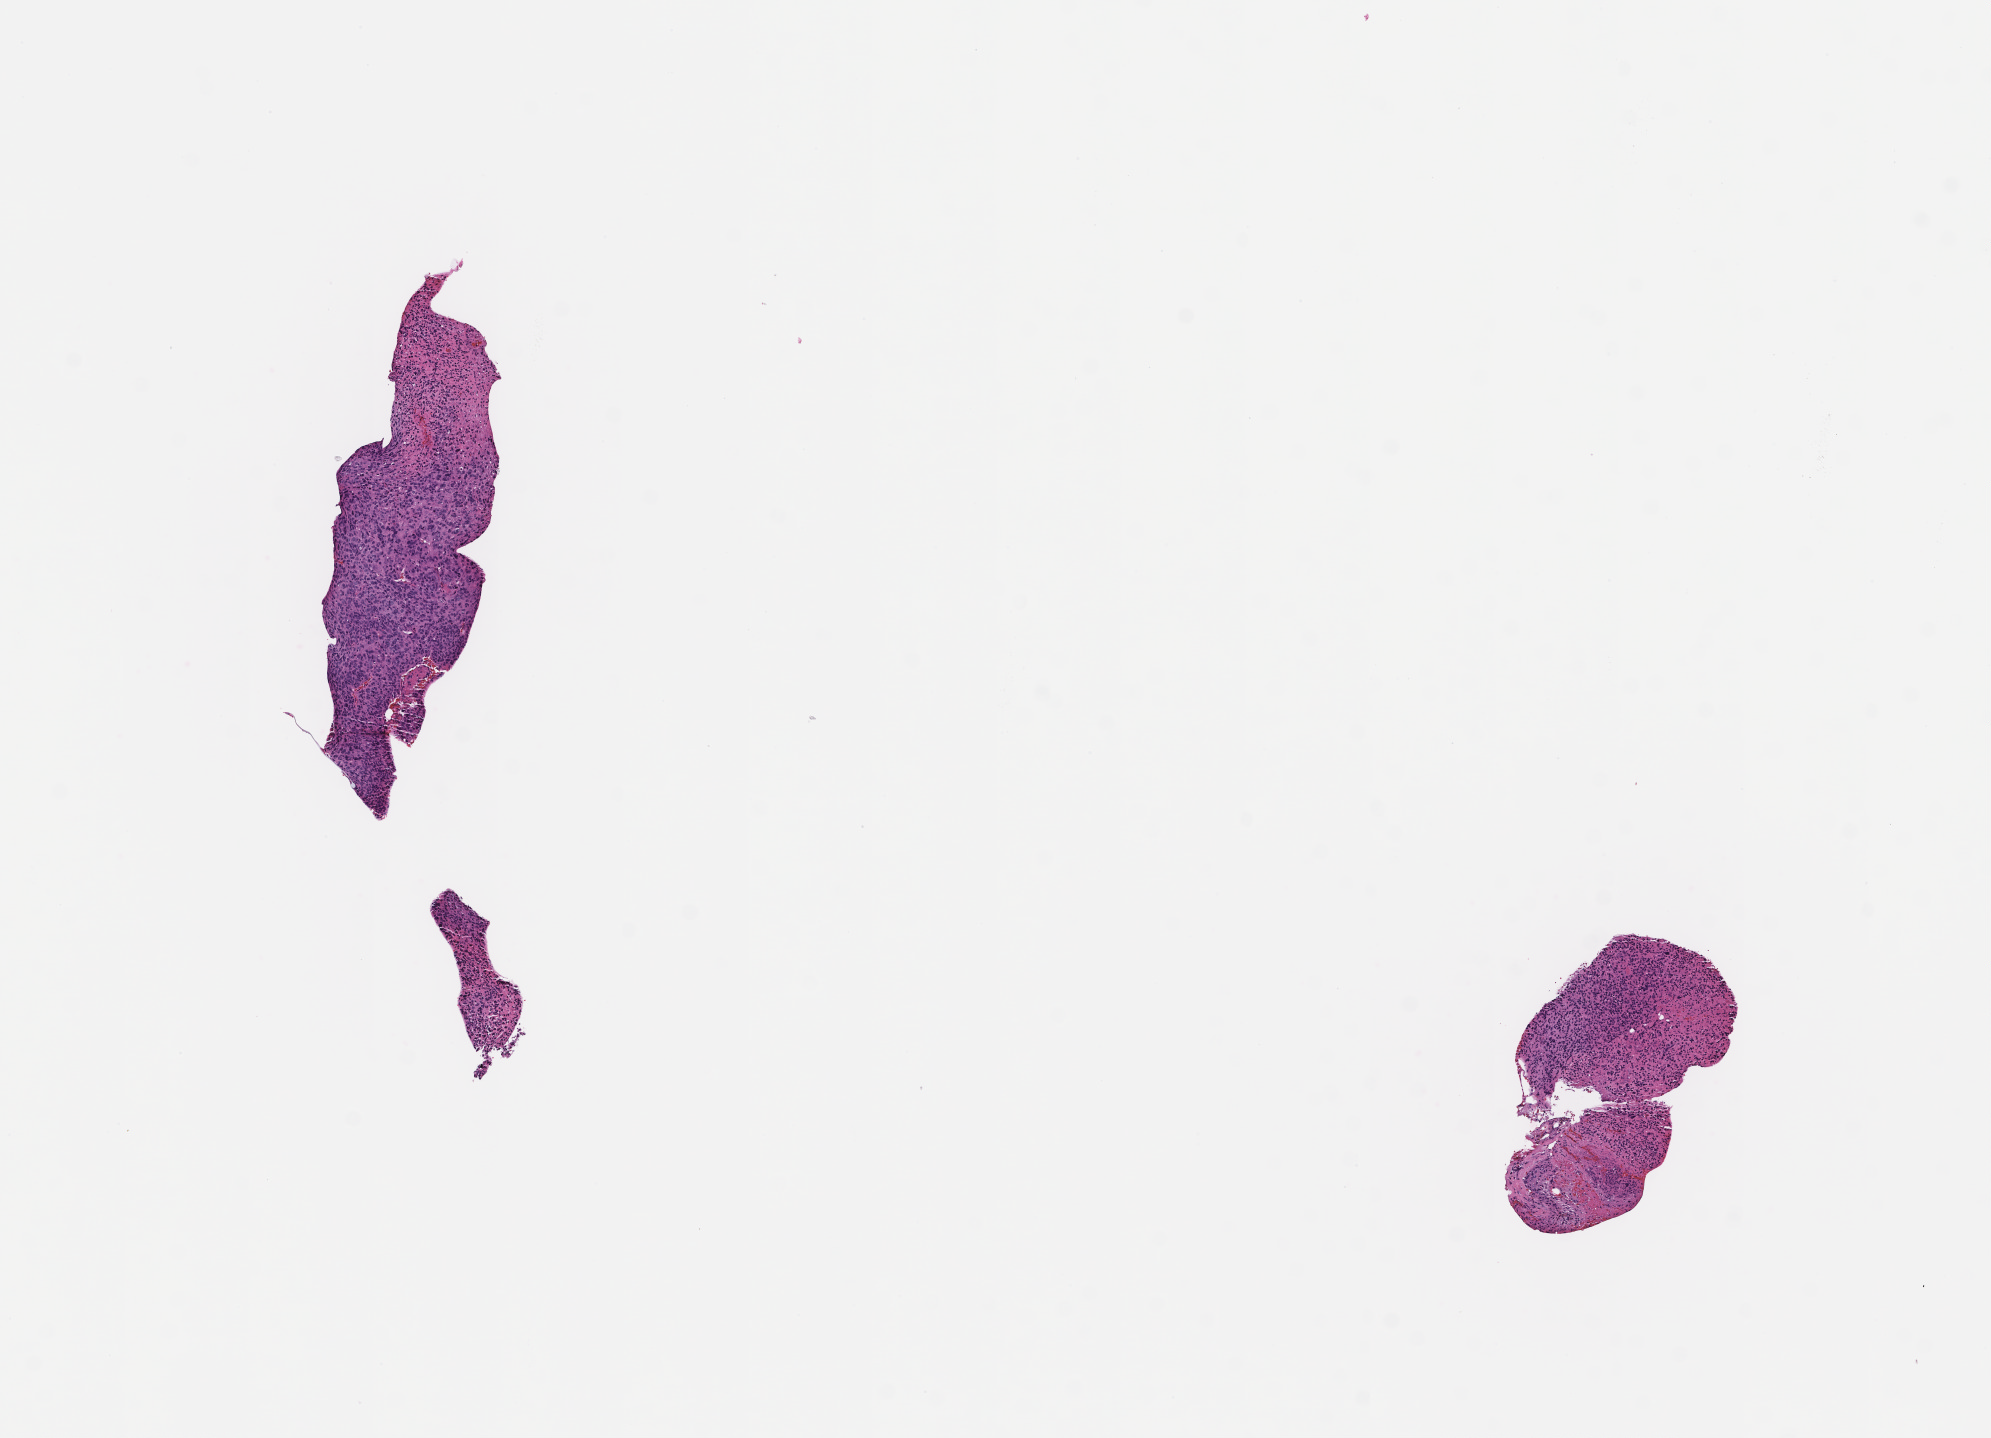
Digitized H&E-stained section — a low-resolution overview of the entire scanned area, about 8.0 x 5.8 mm; formalin-fixed paraffin-embedded section; specimen time point: collected at baseline (before treatment). Patient: female.
This section: metastasis (sampled organ not recorded). Primary diagnosis of the patient: Invasive Breast Carcinoma.